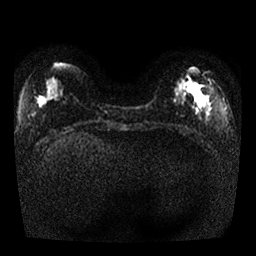
Breast MRI, one axial slice. Slice 8 of 25 in the series (ordered by position). Diffusion-weighted series; image 2 of 4 stored at this slice position (different b-values; order by instance number). 1.5 T. 4 mm slice thickness. 256 × 256 image matrix. Female patient.
Structures marked on this image (outlined manually by an expert reader):
- tumour on diffusion-weighted imaging: bounding box (x1, y1, x2, y2) in pixels: (179, 80, 198, 90)